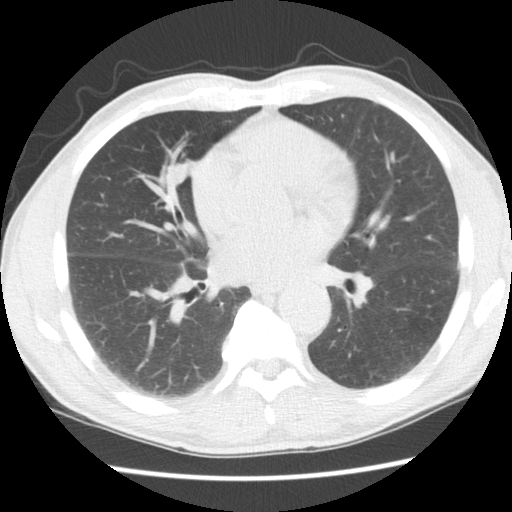
Chest CT (low-dose screening protocol), one axial image; second screening round (one year after baseline); lung window (W 1500 / L -600 HU); 120 kVp; slice 80 of 152 in the series. Male, age 65 years at enrolment. Current smoker at enrolment.
Expert reader's lesion annotation, bounding box [x1, y1, x2, y2] px = [132, 149, 199, 212]. Reader record for this screening exam (exam-level; its link to the box is not recorded): non-calcified nodule or mass ≥4 mm, right middle lobe, 11 × 9 mm, smooth margins, soft tissue attenuation, pre-existing on the prior screen: no. Later outcome: lung cancer diagnosed 601 days after this screen — squamous cell carcinoma, NOS, right middle lobe, poorly differentiated (G3), stage IA (AJCC 6th edition), 23 mm at pathology.